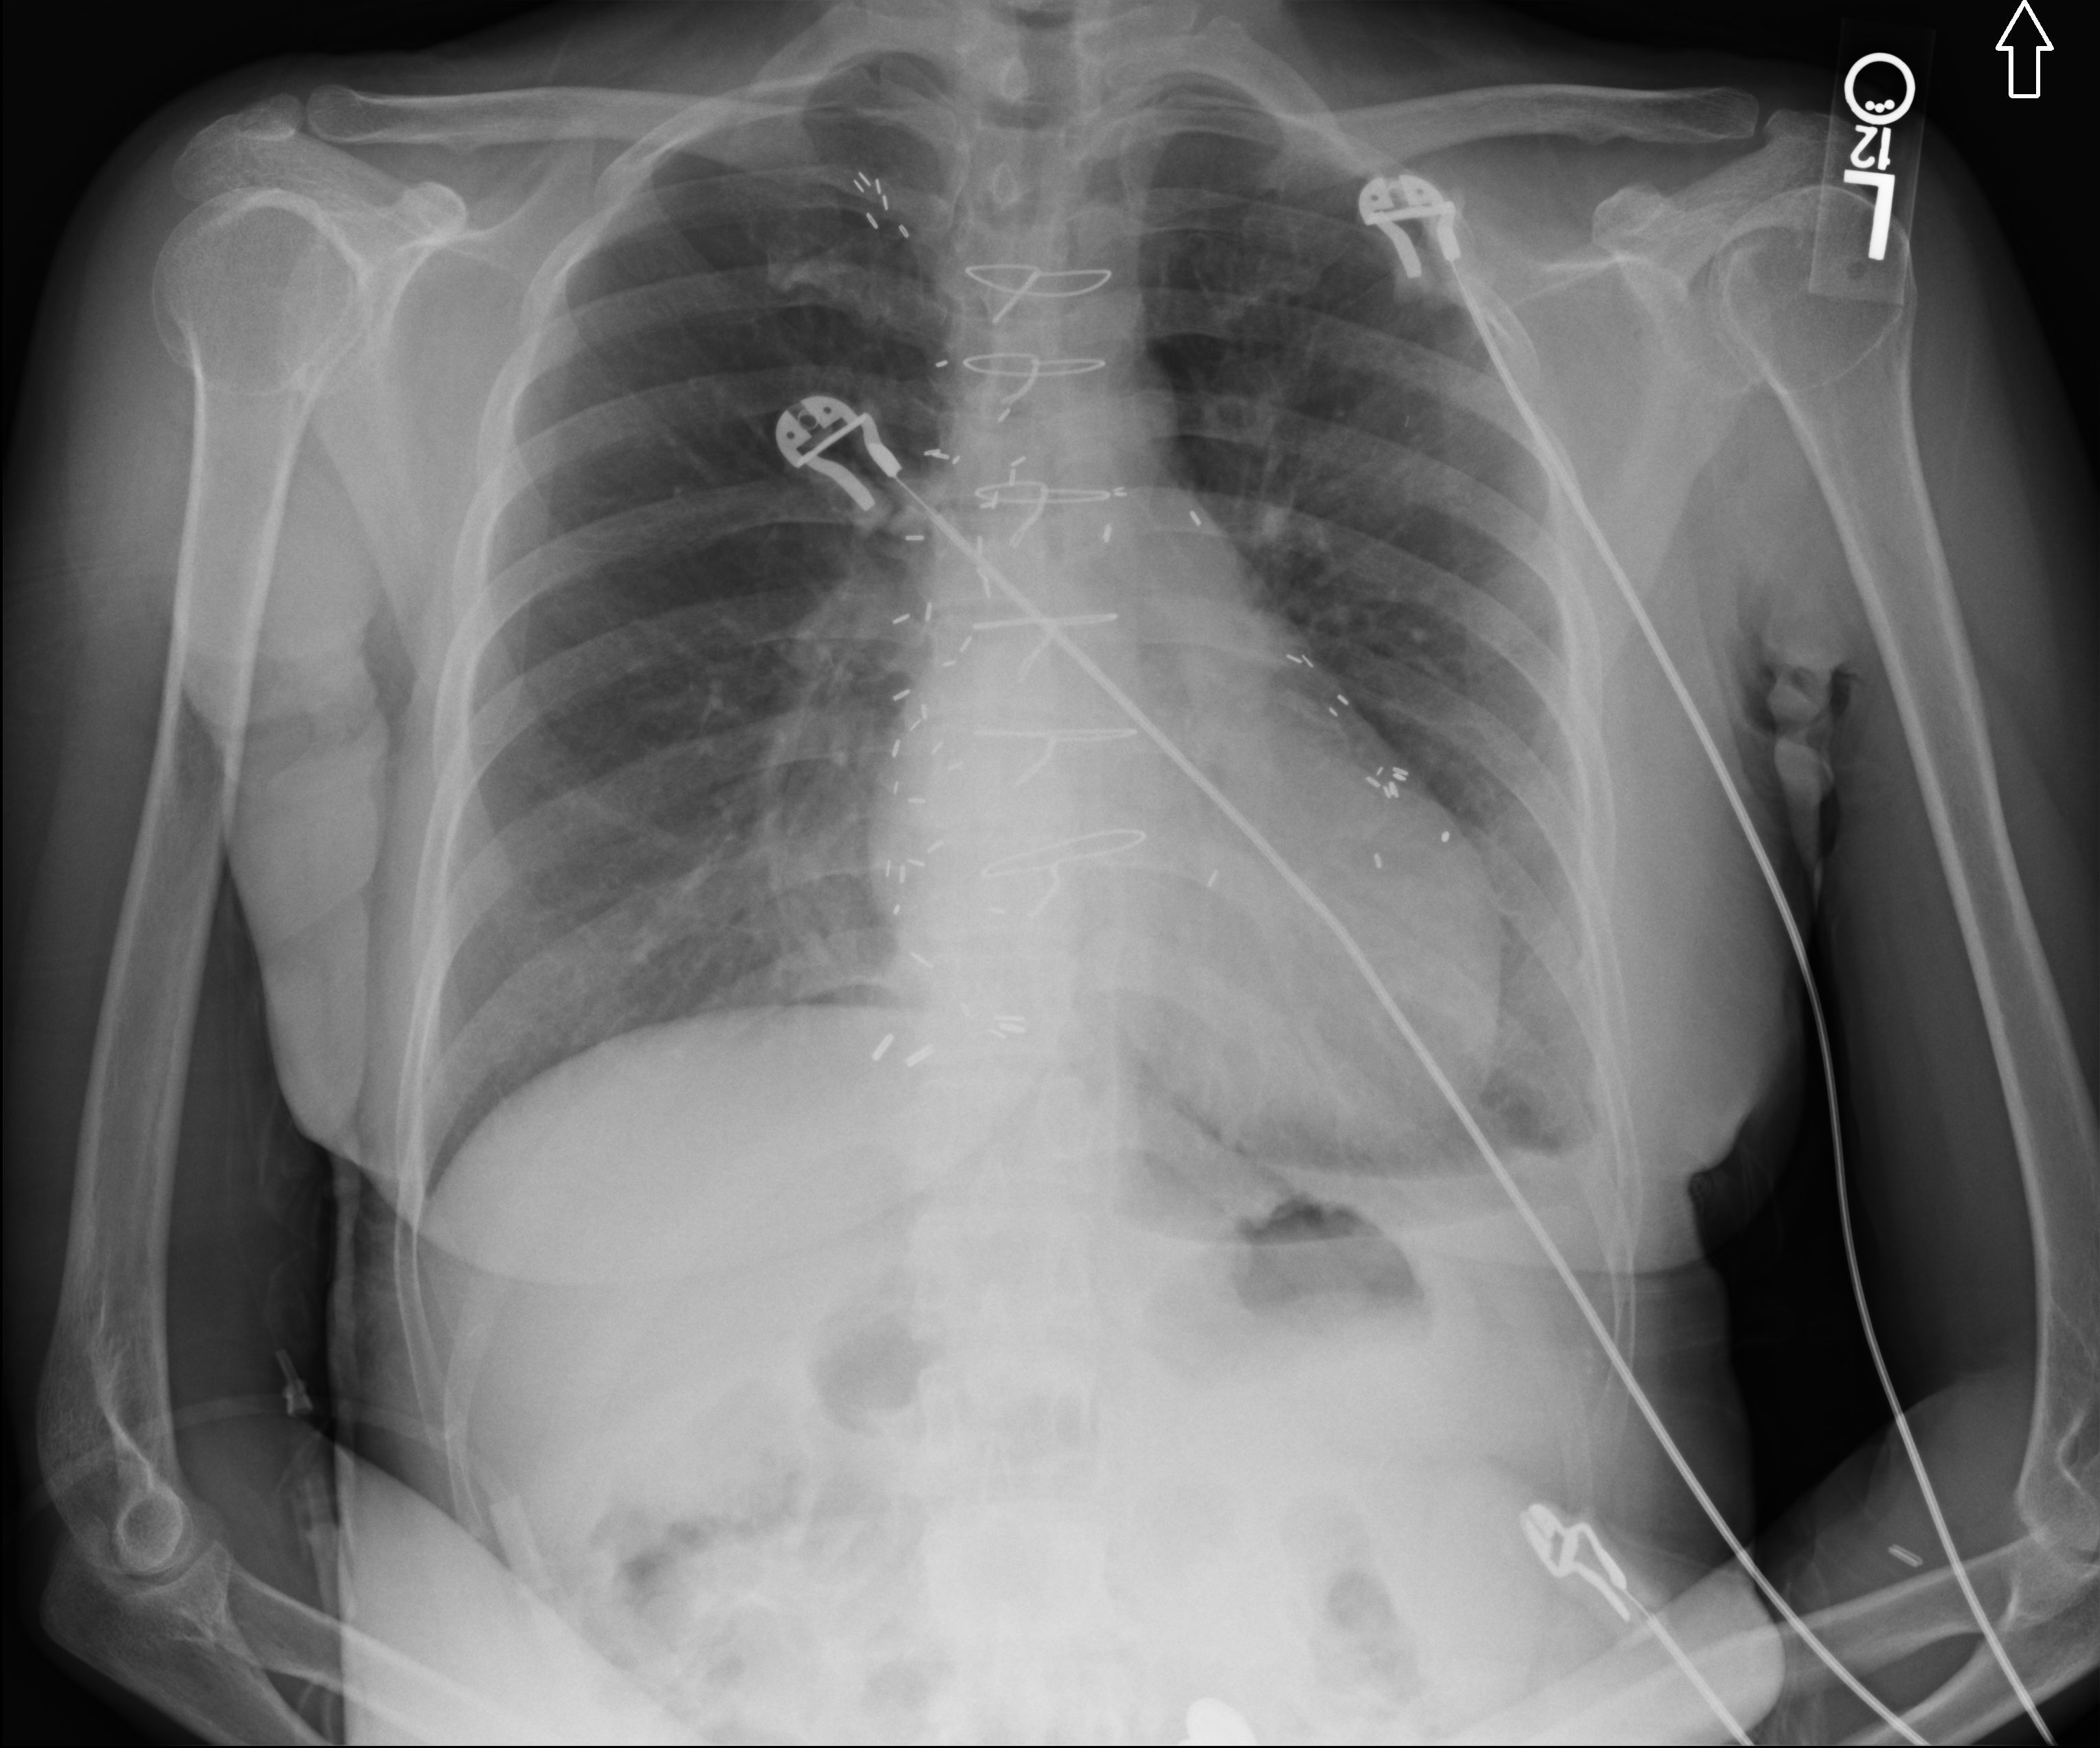
Bedside chest radiograph (computed radiography), anteroposterior (AP) projection. Male patient hospitalised with COVID-19, age 18–59 years.
Admission-level facts for this patient (not findings on this image; timing relative to this image not recorded): mechanically ventilated during this hospital stay: no; admitted to intensive care during this hospital stay: no; chronic kidney disease (admission record): yes.